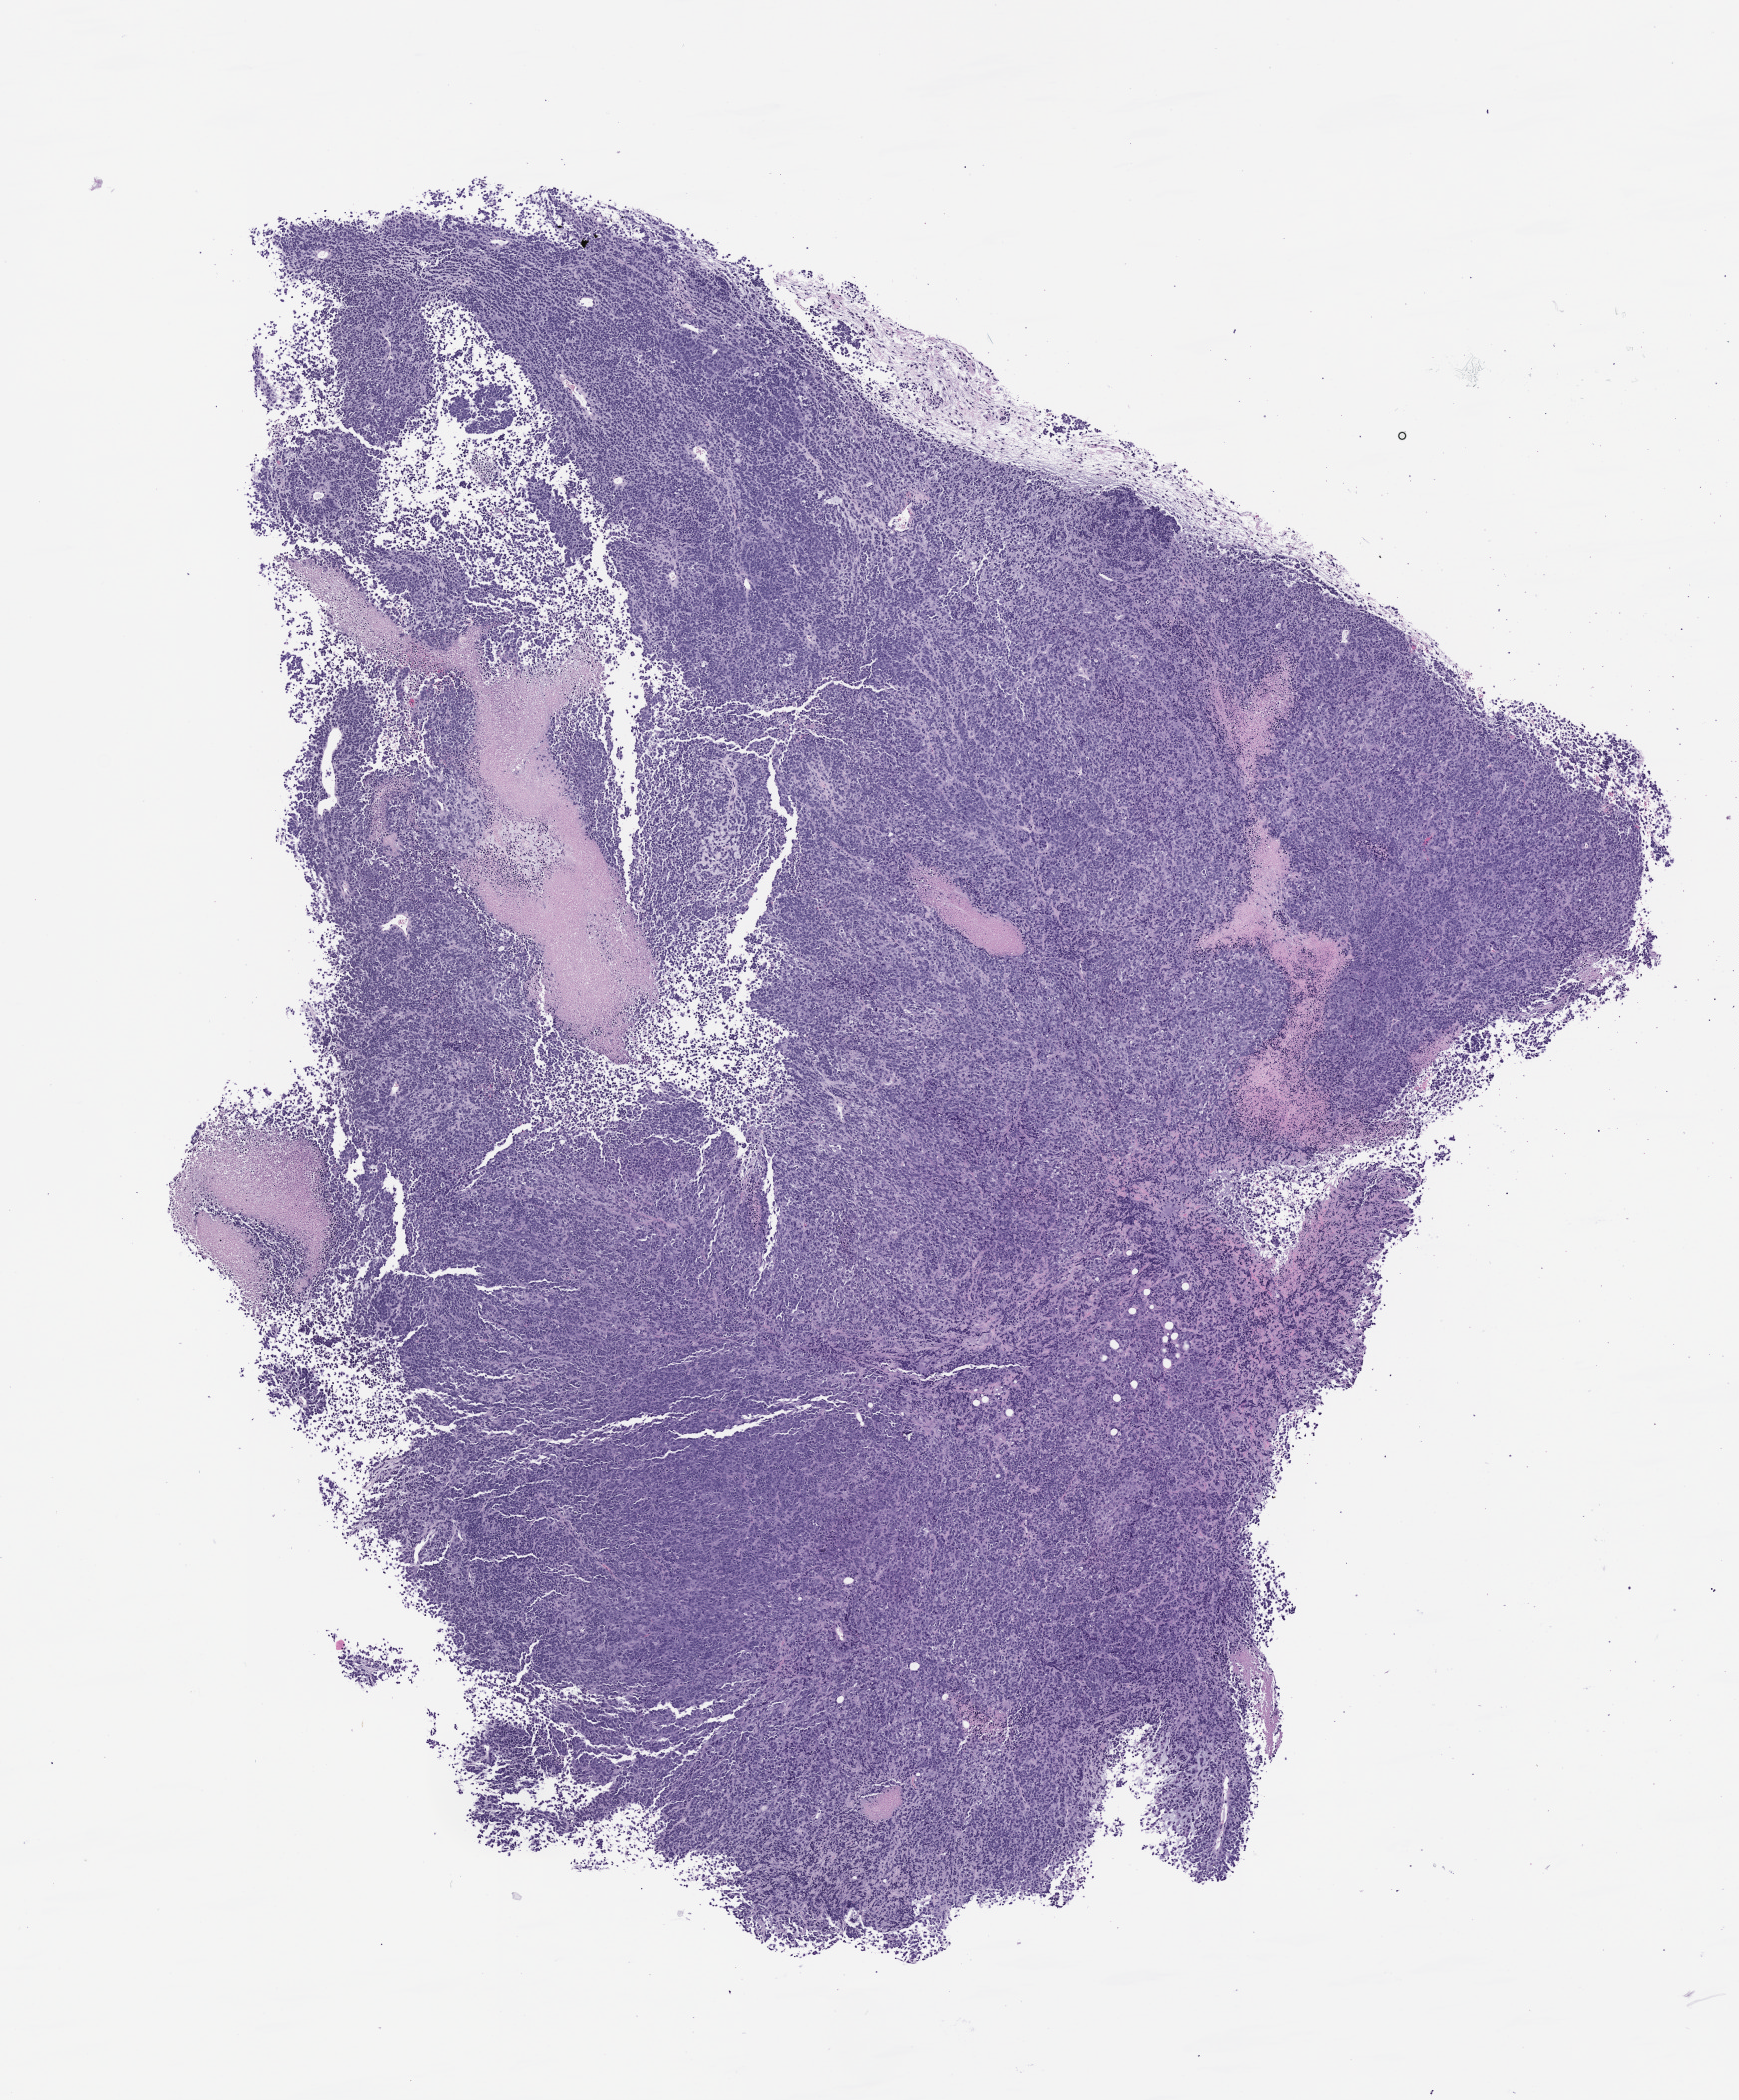
Hematoxylin and eosin (H&E) whole-slide image of a patient-derived xenograft (PDX) tumor grown in a mouse, passage 0, a low-resolution overview of the entire scanned area, about 7.0 x 8.5 mm, FFPE section, tumor site category: uterus.
Originating patient diagnosis: Carcinosarcoma.